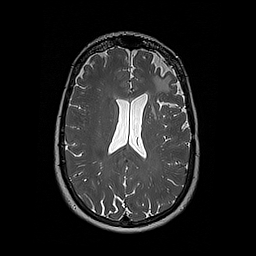
Brain MRI from a brain-tumour surgery series, one axial slice; position 112 of 192 along the scan axis; 1 mm slice thickness; 256 × 256 image matrix, field of view 250 × 250 mm. From the clinical record (not read from this slice): histopathology: Oligodendroglioma; WHO grade: 2; IDH mutation: yes.
Outlined on this slice (manually delineated by an expert):
- tumour: bounding box (x1, y1, x2, y2) in pixels: (152, 76, 162, 114)